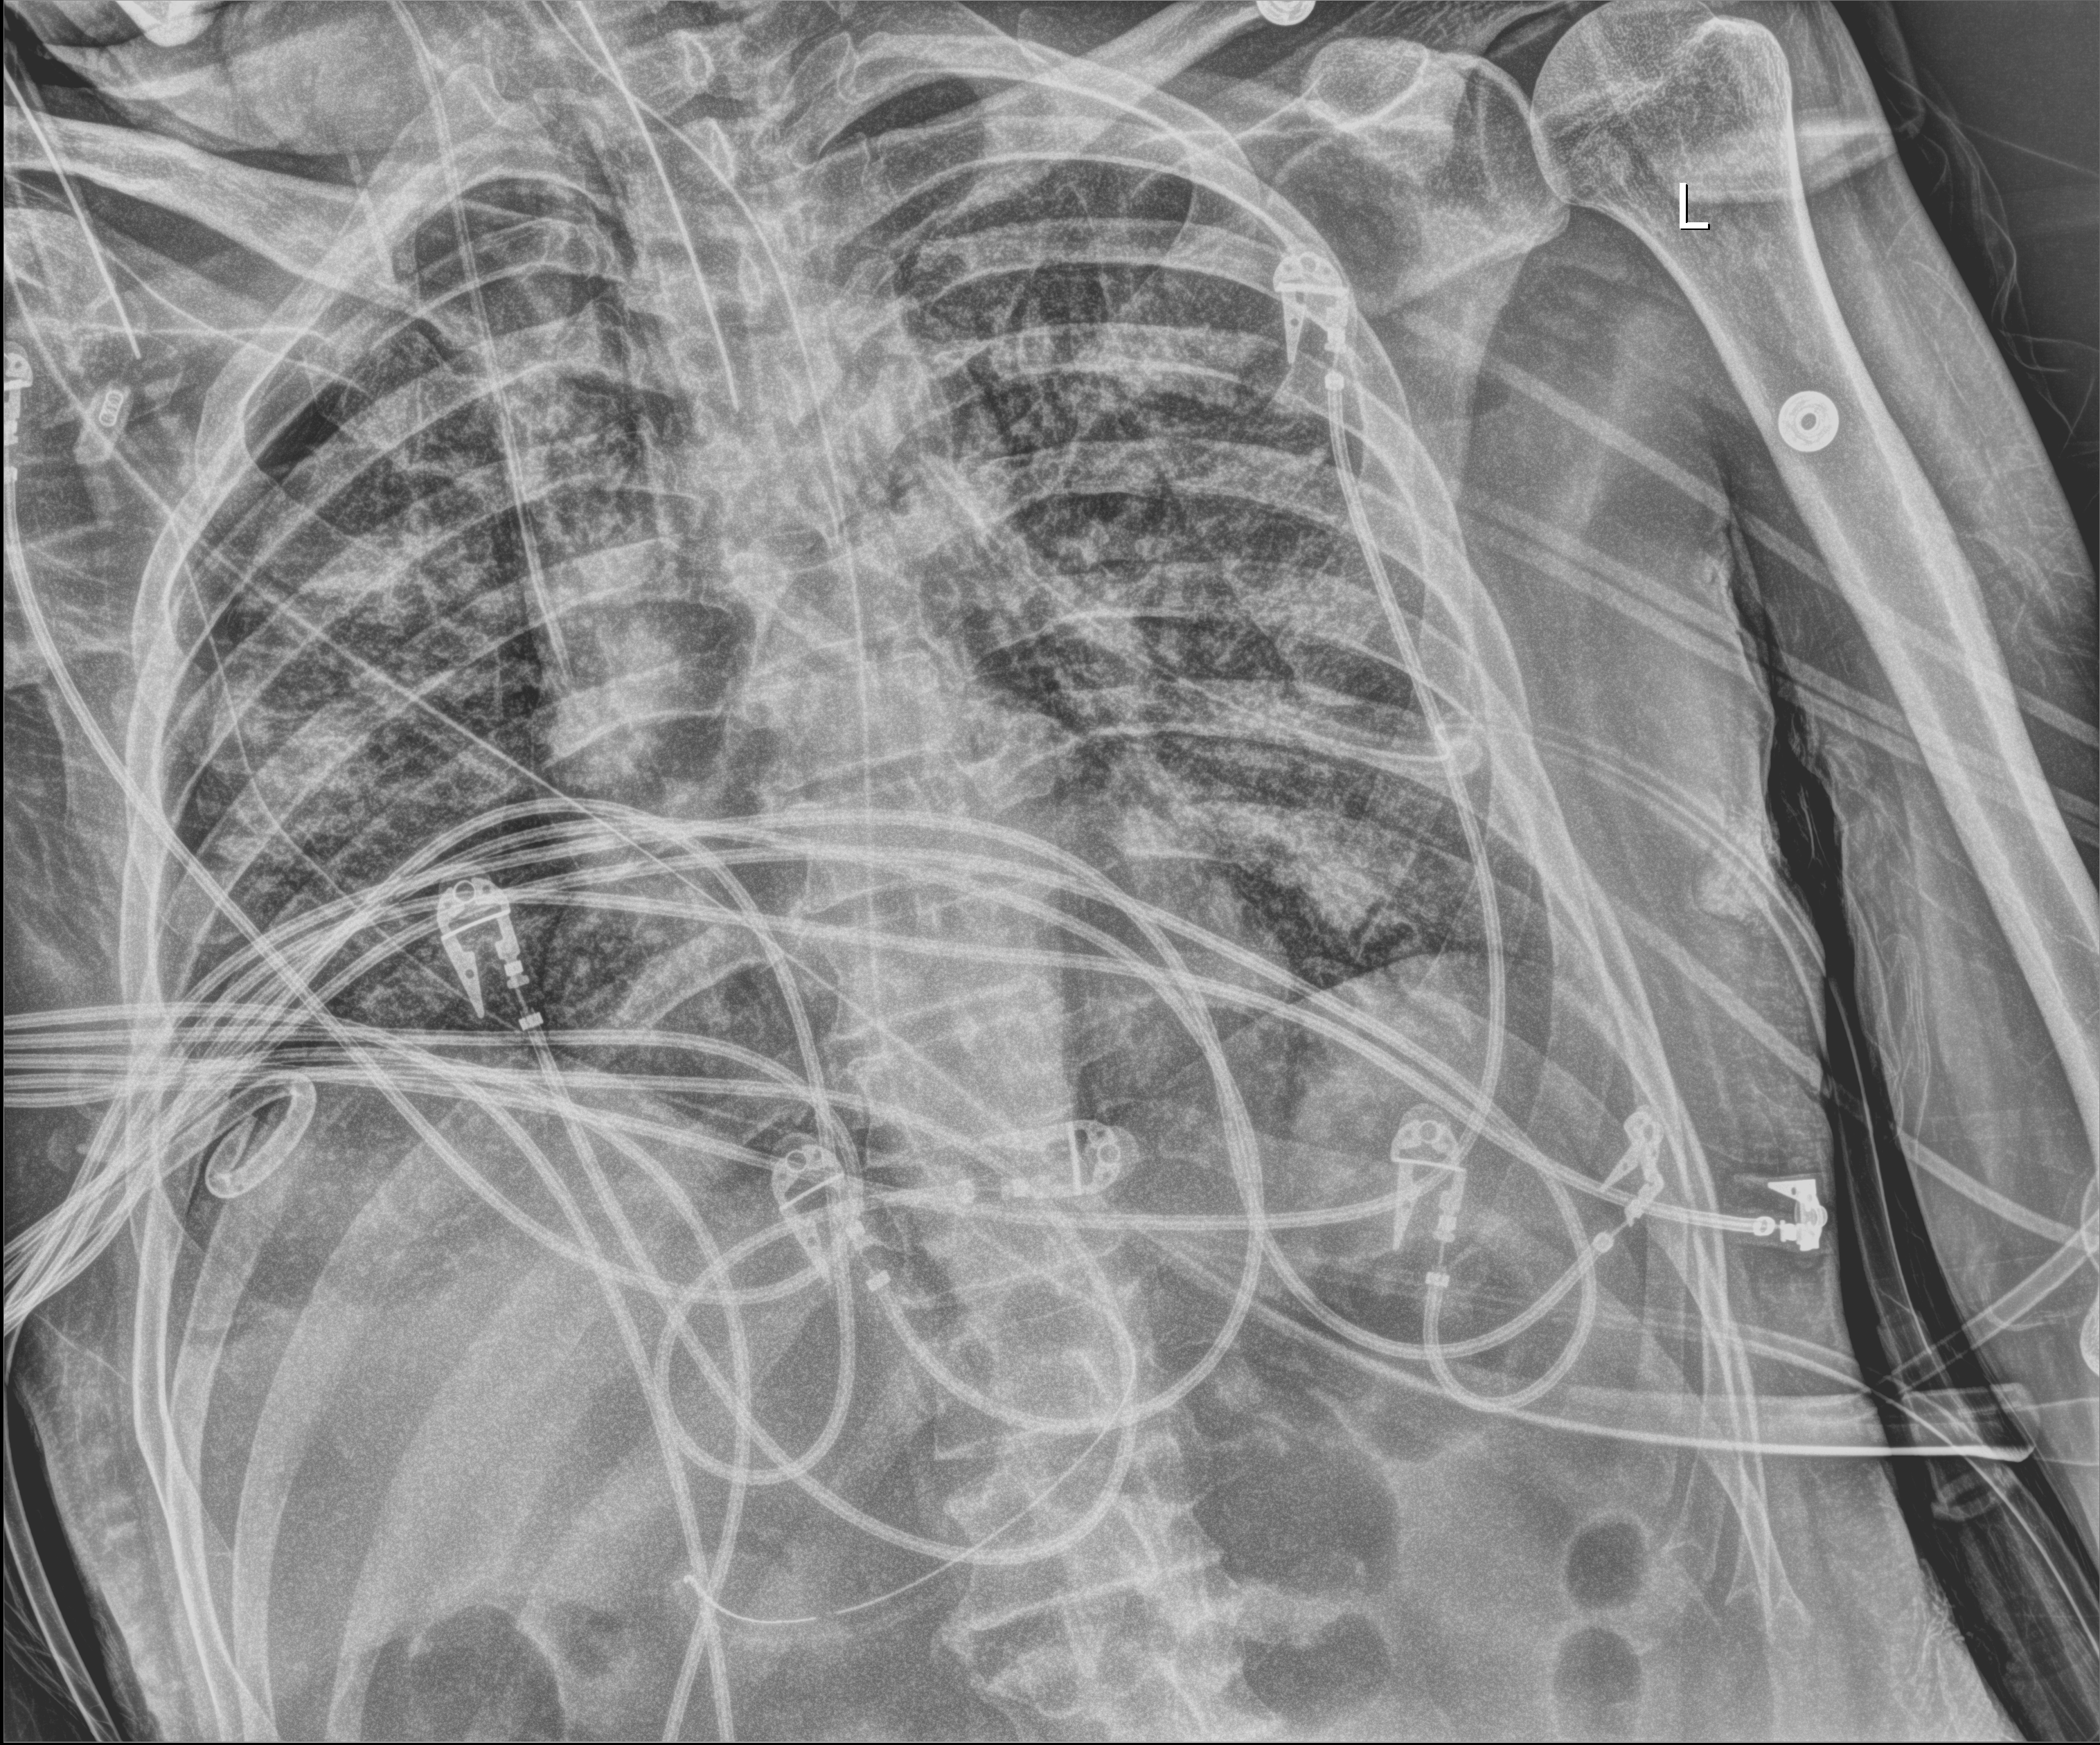
Bedside chest radiograph (digital radiography); anteroposterior (AP) projection. Patient hospitalised with COVID-19; male, aged 18–59 years.
Admission-level facts for this patient (not findings on this image; timing relative to this image not recorded): diabetes (admission record): no.